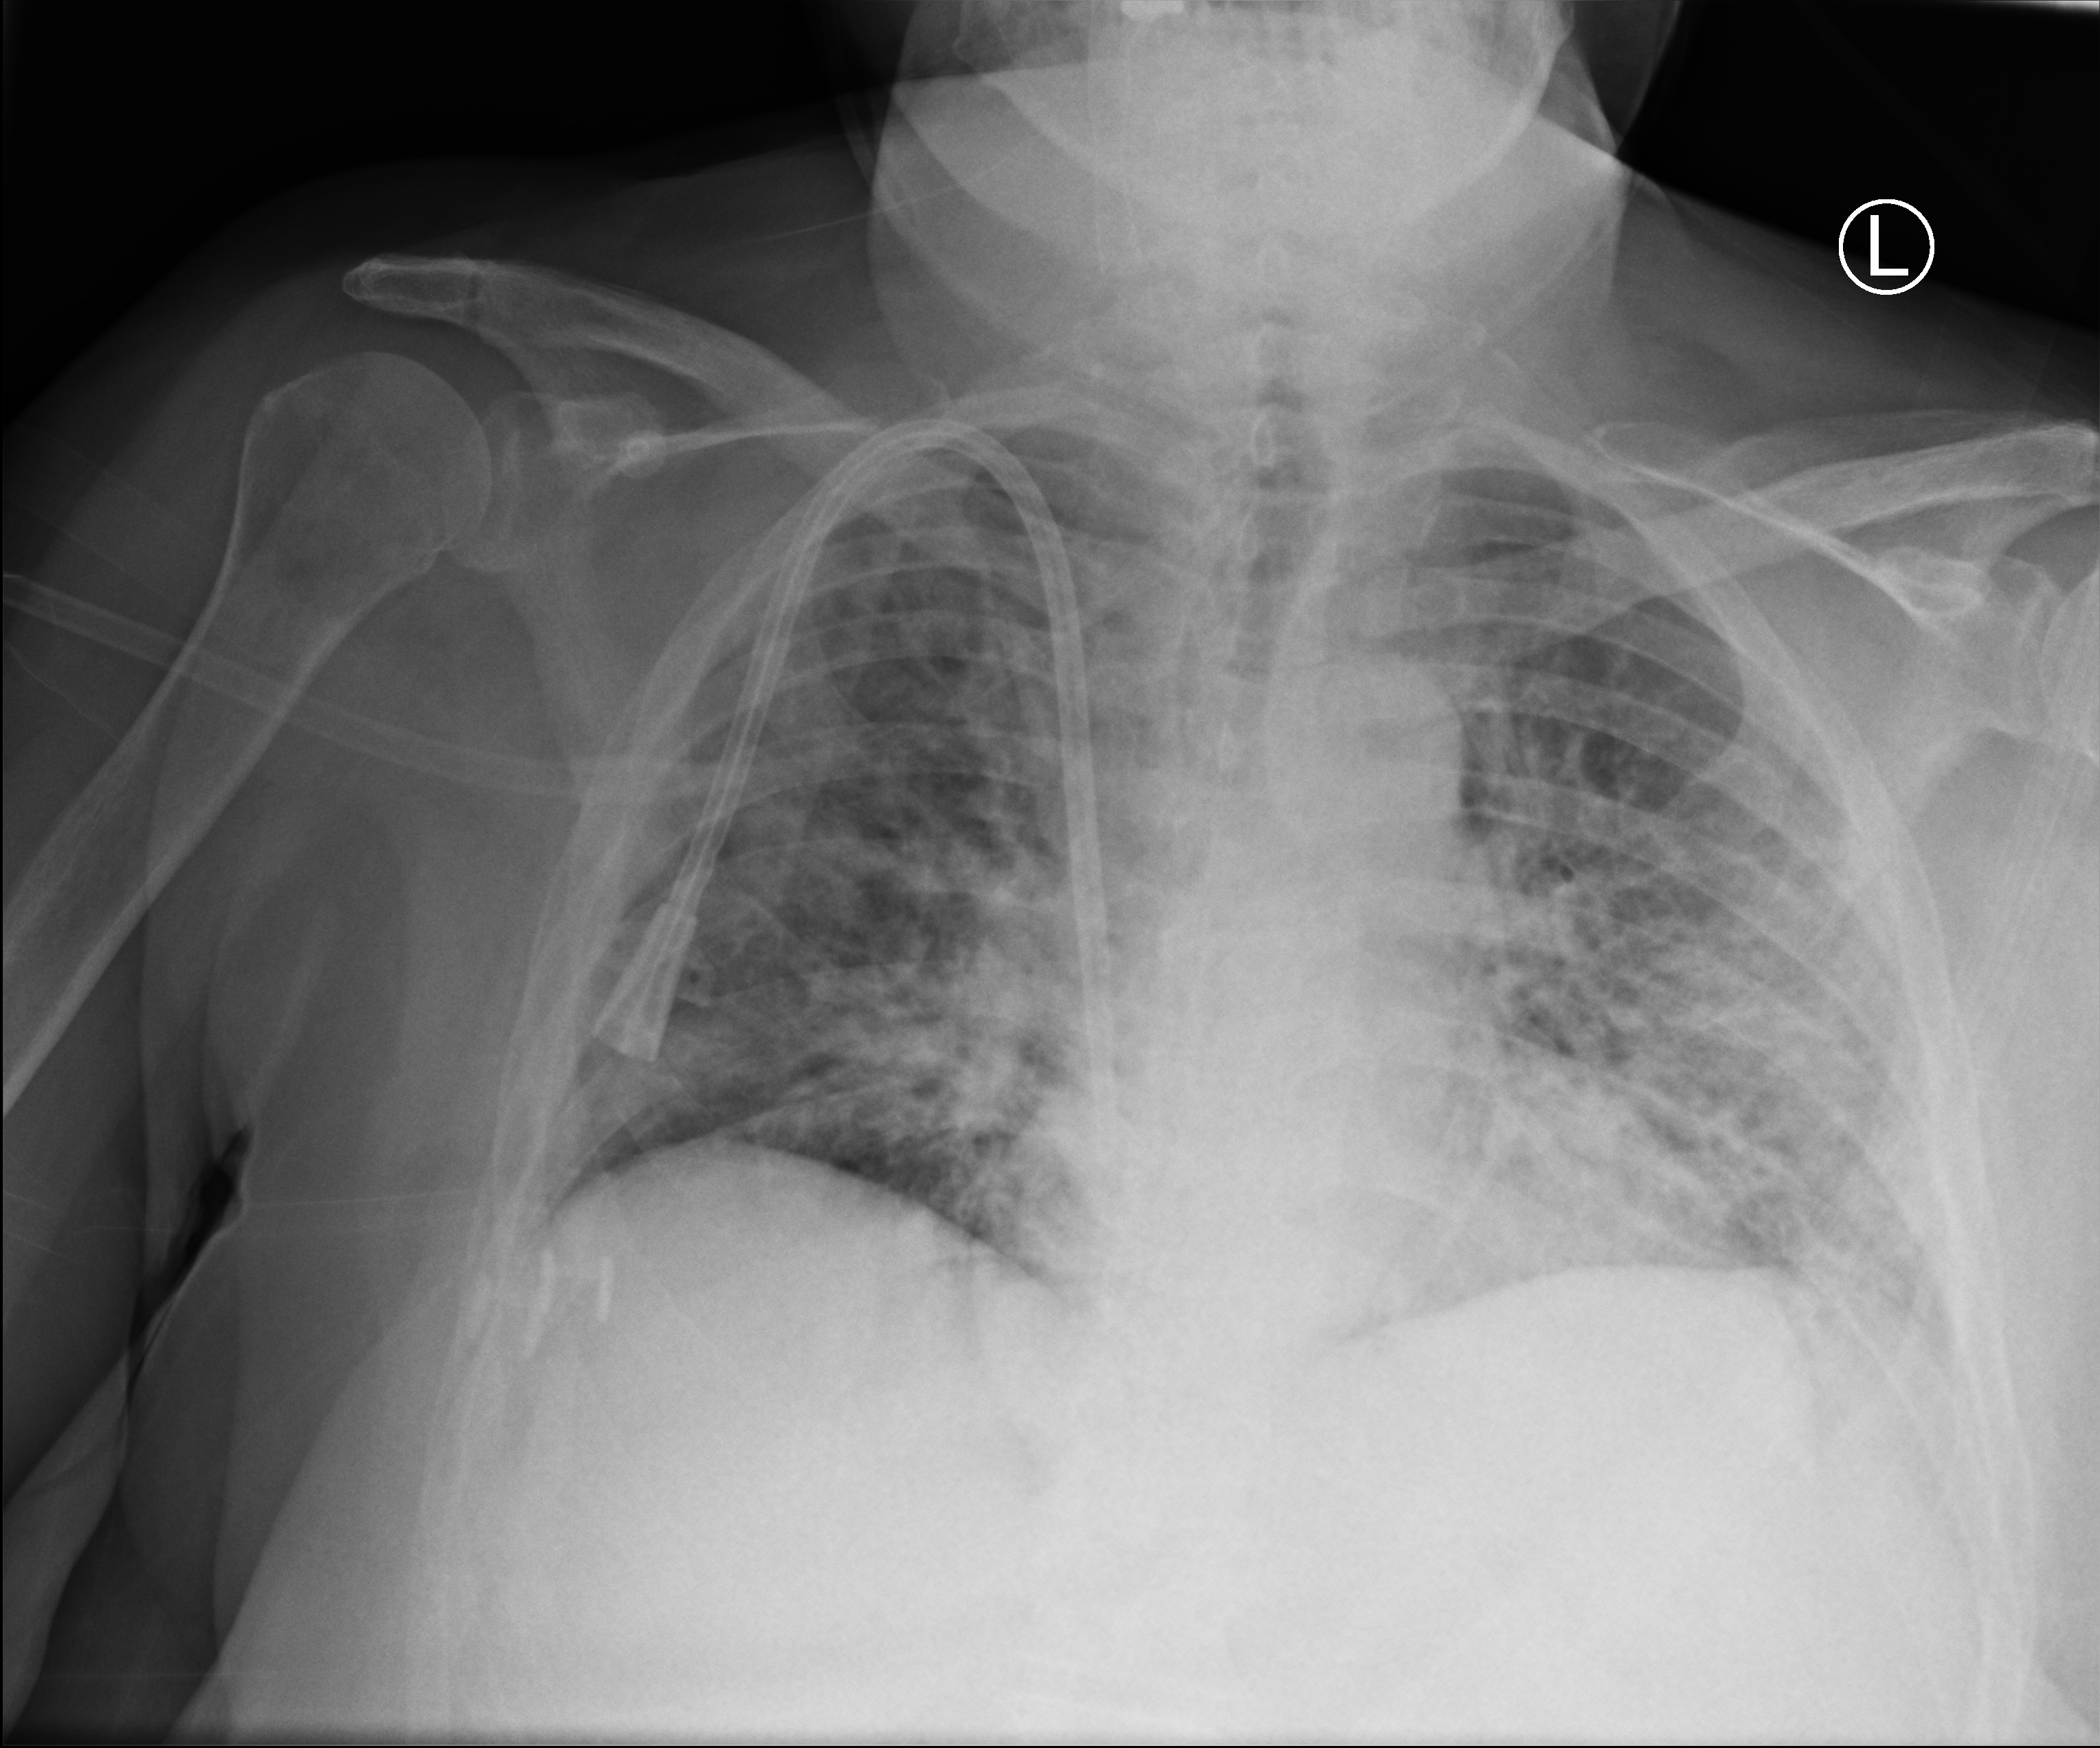
Chest X-ray (portable); anteroposterior (AP) projection. Female patient hospitalised with COVID-19, age 60–74 years.
Admission-level facts for this patient (not findings on this image; timing relative to this image not recorded):
- length of hospital stay: 8 days
- admitted to intensive care during this hospital stay: no
- mechanically ventilated during this hospital stay: no